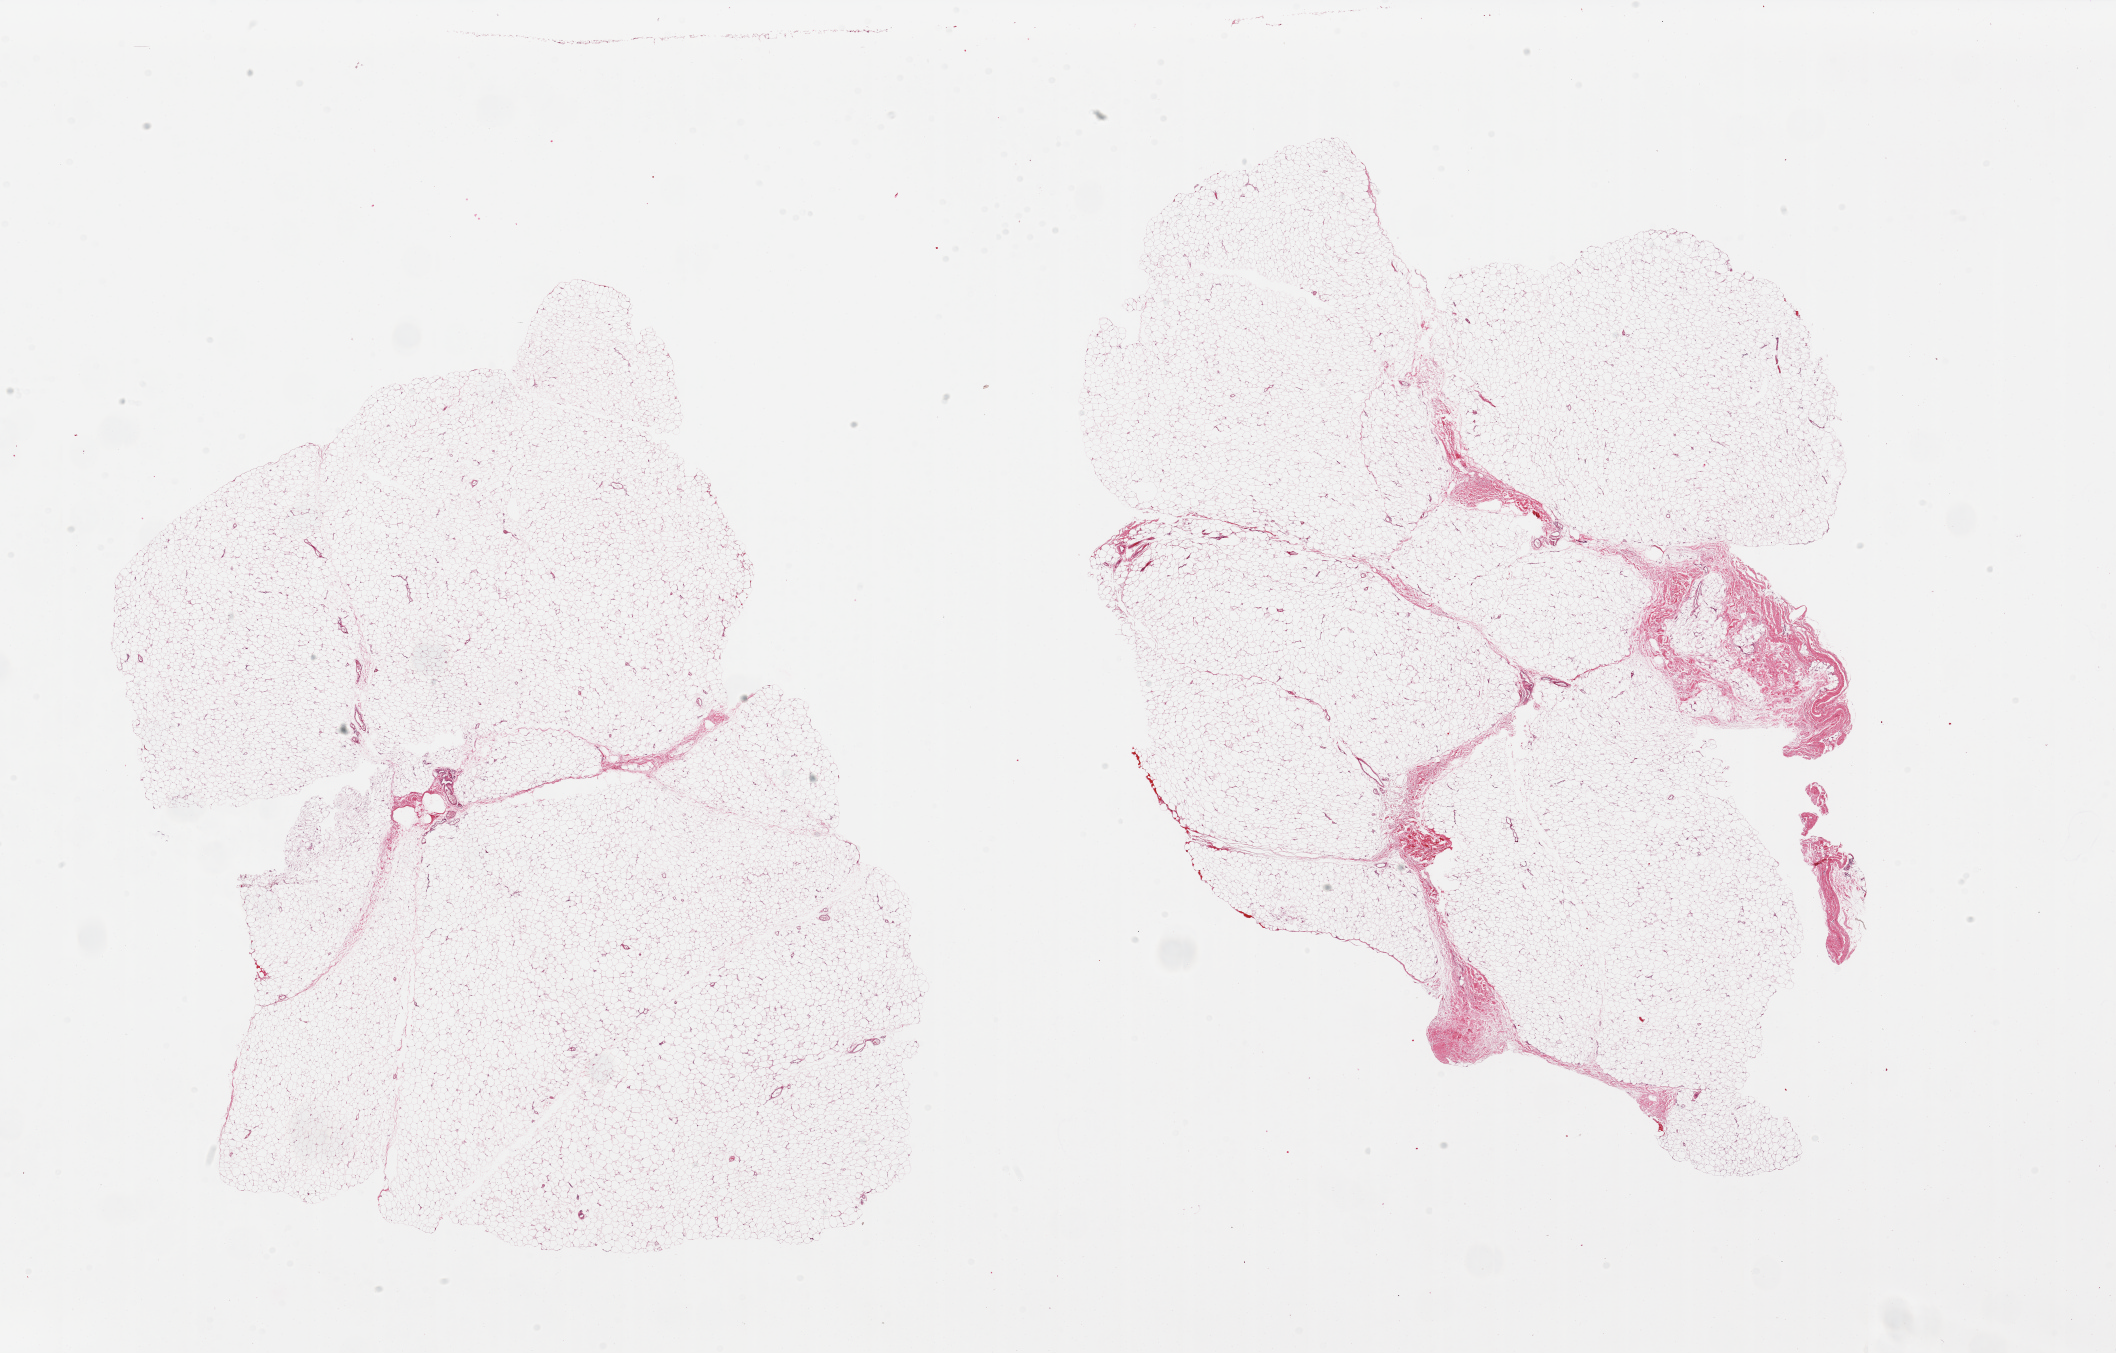
Hematoxylin and eosin (H&E) whole-slide image, brightfield — shown as a low-resolution overview of the whole scanned area (about 33.5 x 21.4 mm, slide scanned at 20x). PAXgene-fixed paraffin-embedded (PFPE) section. Target tissue: adipose tissue. Donor tissue sample. Donor sex: female.
Pathologist's review note for this sample: 2 pieces. Large size needed refixing.